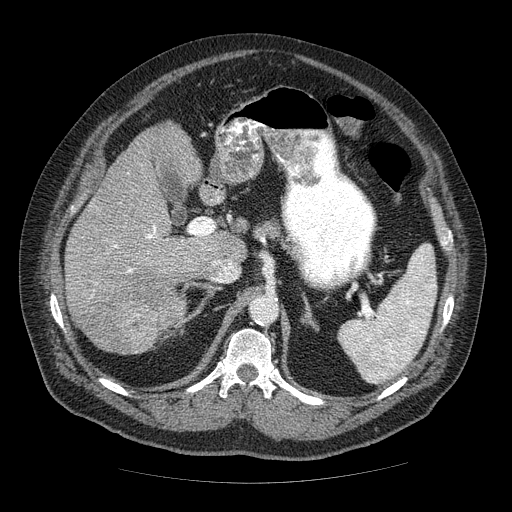
Contrast-enhanced abdominal CT (liver protocol), one axial slice; reconstruction kernel STANDARD; 120 kVp; soft-tissue window (W 400 / L 40 HU); 512 × 512 image matrix. Case-level facts recorded for this patient, not image findings: diagnosis: hepatocellular carcinoma (patient treated with transarterial chemoembolisation; whether this scan precedes or follows treatment is not stated here); TNM stage (as recorded): Stage-IIIA; Child-Pugh class: A; tumour size: 7 cm.
Outlined on this slice (semi-automatic segmentation, software-assisted and operator-edited):
- liver parenchyma outside the tumour (the mass and vessels are separate outlines, so this box may not span the whole liver): bounding box [x1, y1, x2, y2] px = [66, 122, 246, 346]
- mass: [86, 270, 185, 355]
- liver vessels: [91, 224, 212, 297]